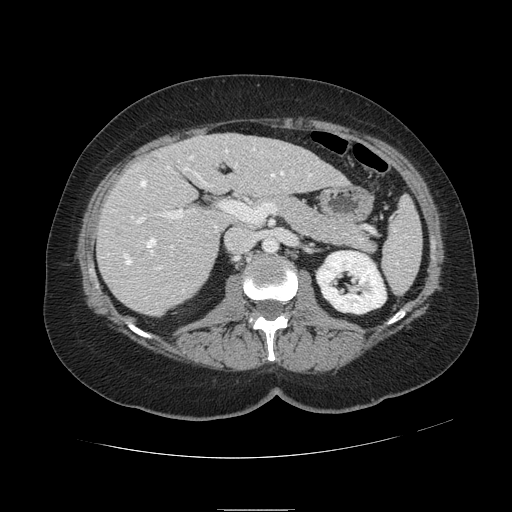
Contrast-enhanced abdominal CT, one axial slice. Slice 50 of 121 in the series (ordered by position). 120 kVp. Soft-tissue window (W 400 / L 40 HU). 512 × 512 image matrix. Female patient, age 52 years. Case-level facts recorded for this patient, not image findings: diagnosis: colorectal cancer liver metastases, imaged before liver resection; multiple liver metastases: yes; largest metastasis: 6.3 cm; chemotherapy before resection: yes.
Outlined on this slice (manually delineated by an expert):
- hepatic veins: bounding box [x1, y1, x2, y2] px = [124, 149, 312, 292]
- liver: [99, 134, 345, 315]
- planned liver remnant (the part of the liver to remain after resection): [172, 134, 346, 196]
- portal vein (with intrahepatic branches): [131, 164, 293, 269]